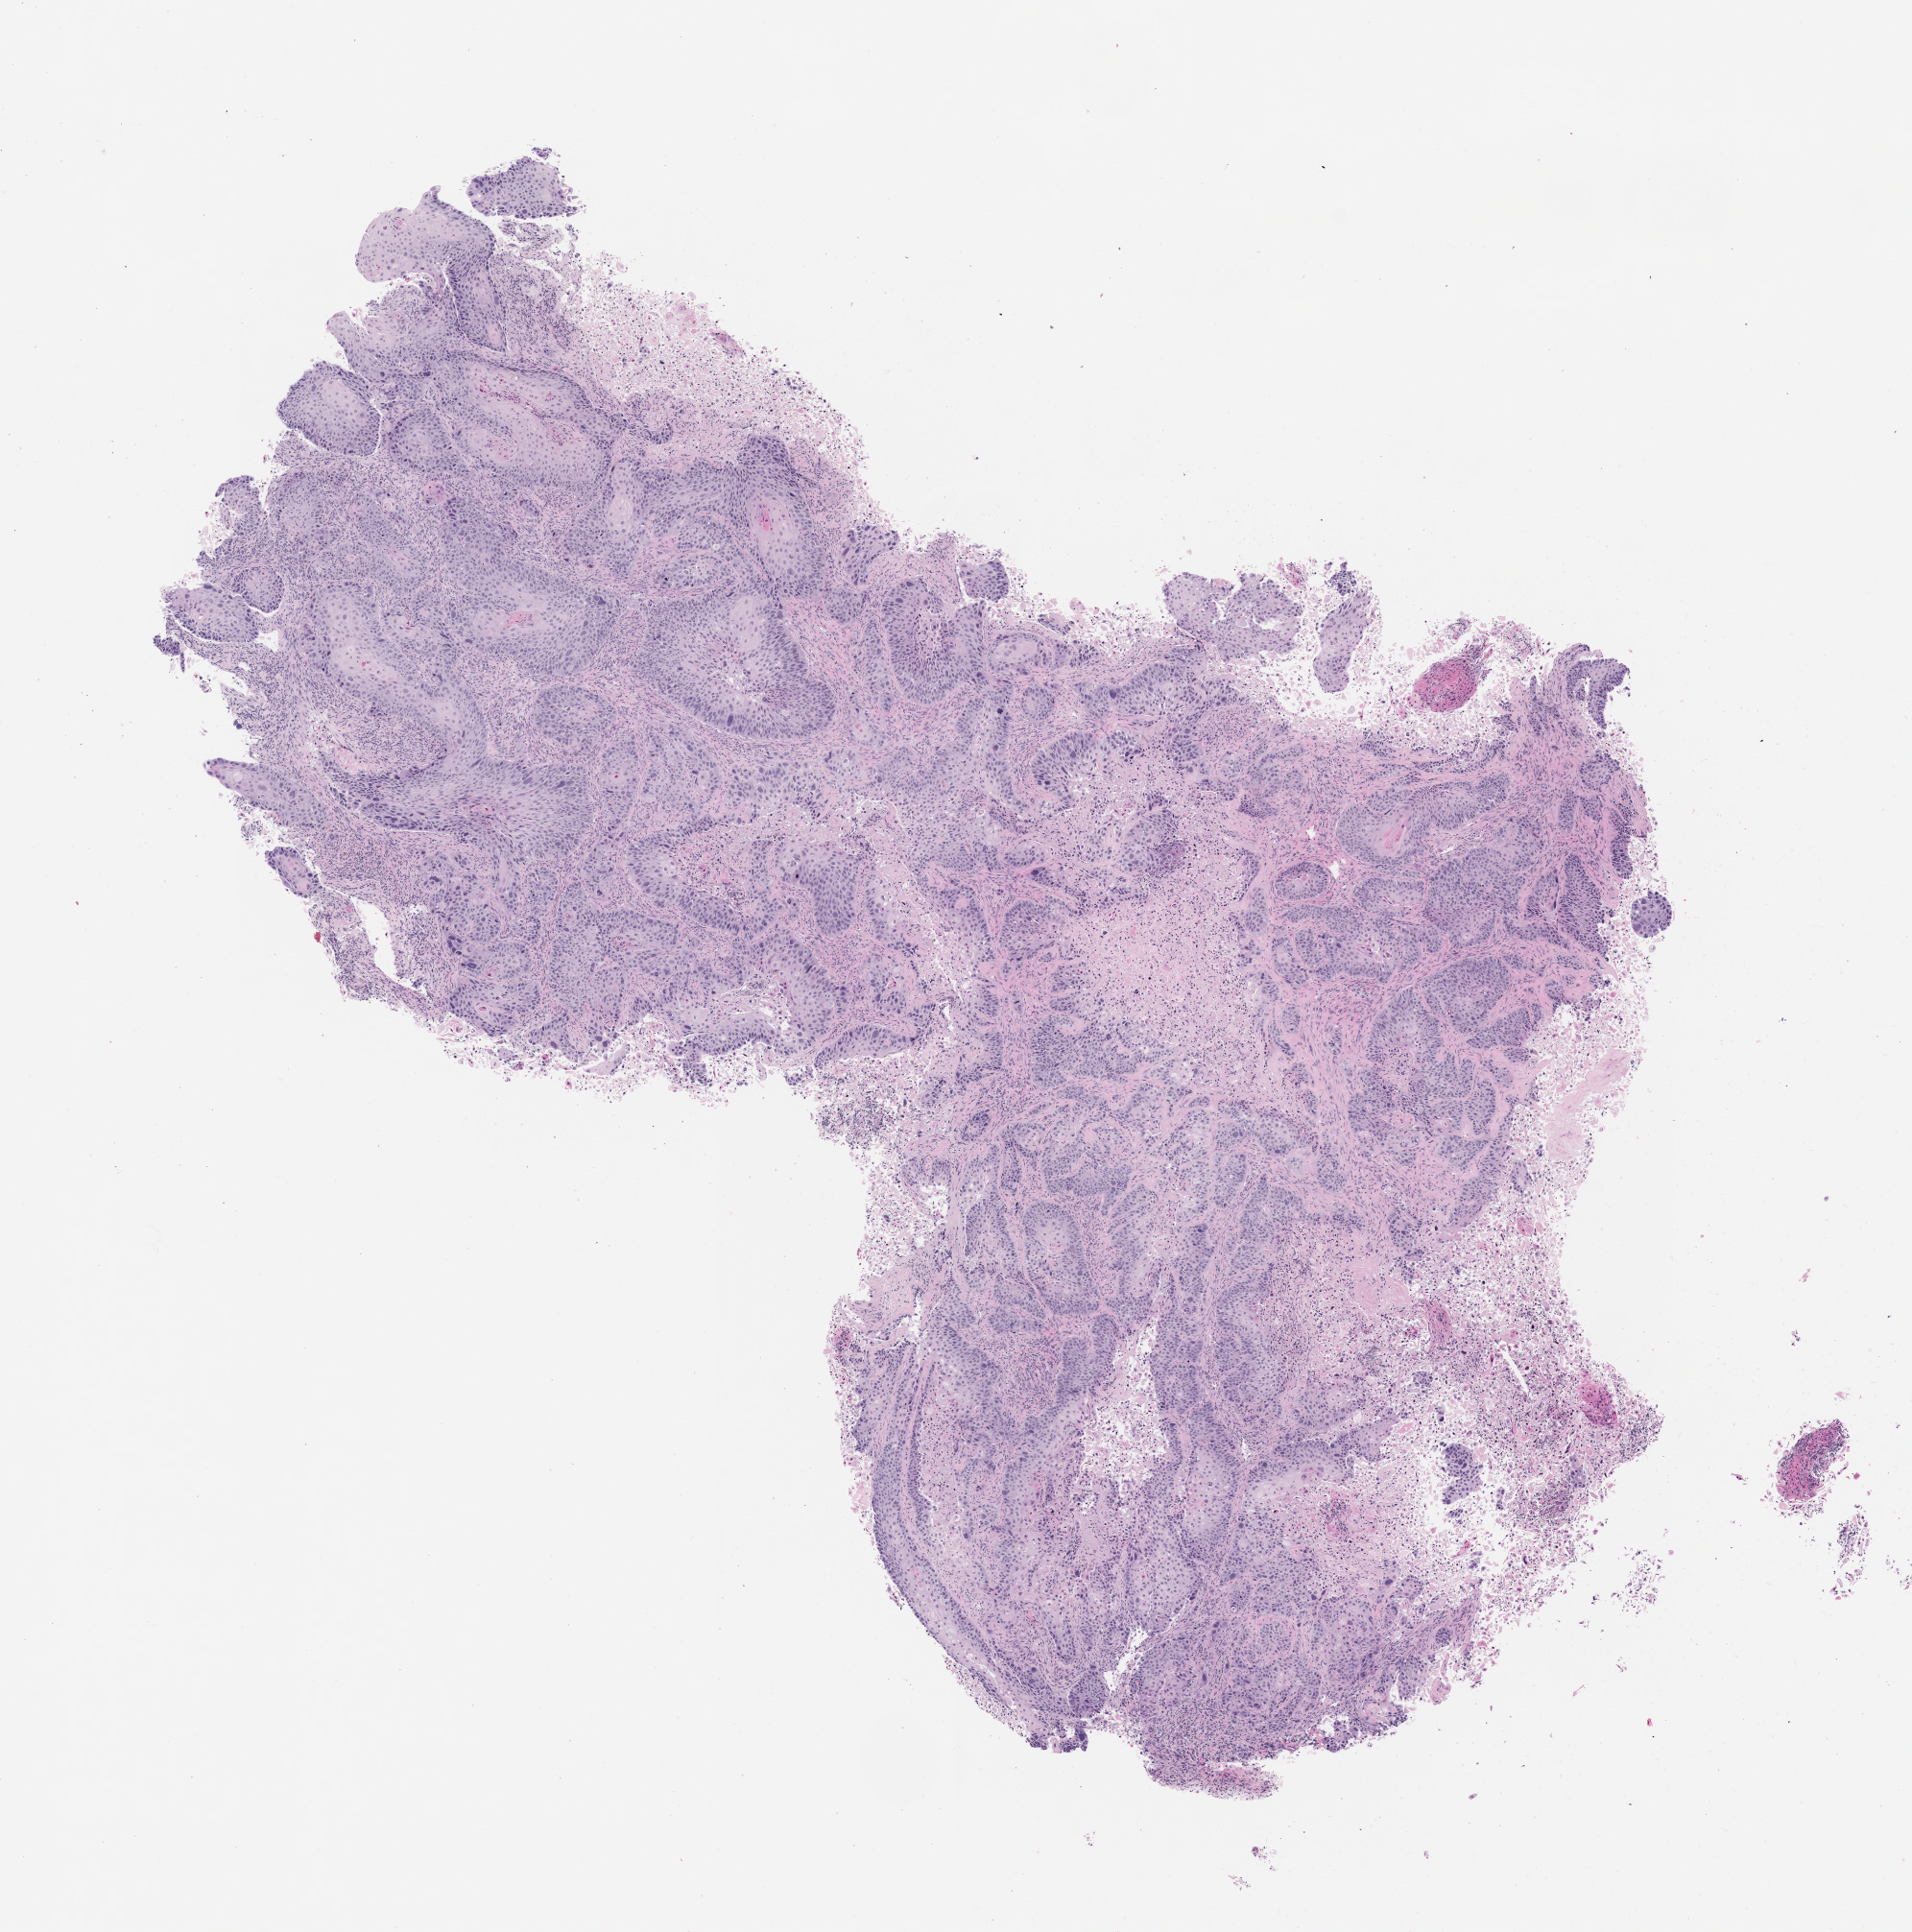
Whole-slide image, haematoxylin and eosin: patient-derived xenograft (human tumor grown in a mouse), passage 1, whole scanned area (about 8.0 x 8.1 mm) shown as a low-resolution overview; FFPE section; tumor site category: lung.
Originating patient diagnosis: Lung Squamous Cell Carcinoma.